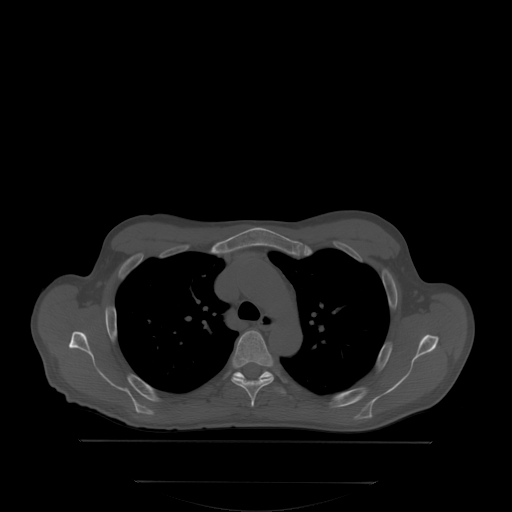
CT including the spine, one axial slice; slice 255 of 350 in the series (ordered by position); bone window (W 1800 / L 400 HU); 512 × 512 image matrix, field of view 500 × 500 mm. Patient: male, 58 years. From the clinical record (not read from this slice): primary cancer: prostate.
Annotated regions visible in this slice (semi-automatic segmentation, software-assisted and operator-edited):
- T4 vertebra: bounding box <232,330,273,406> (left, top, right, bottom; pixels)
- T5 vertebra: <232,371,272,381>